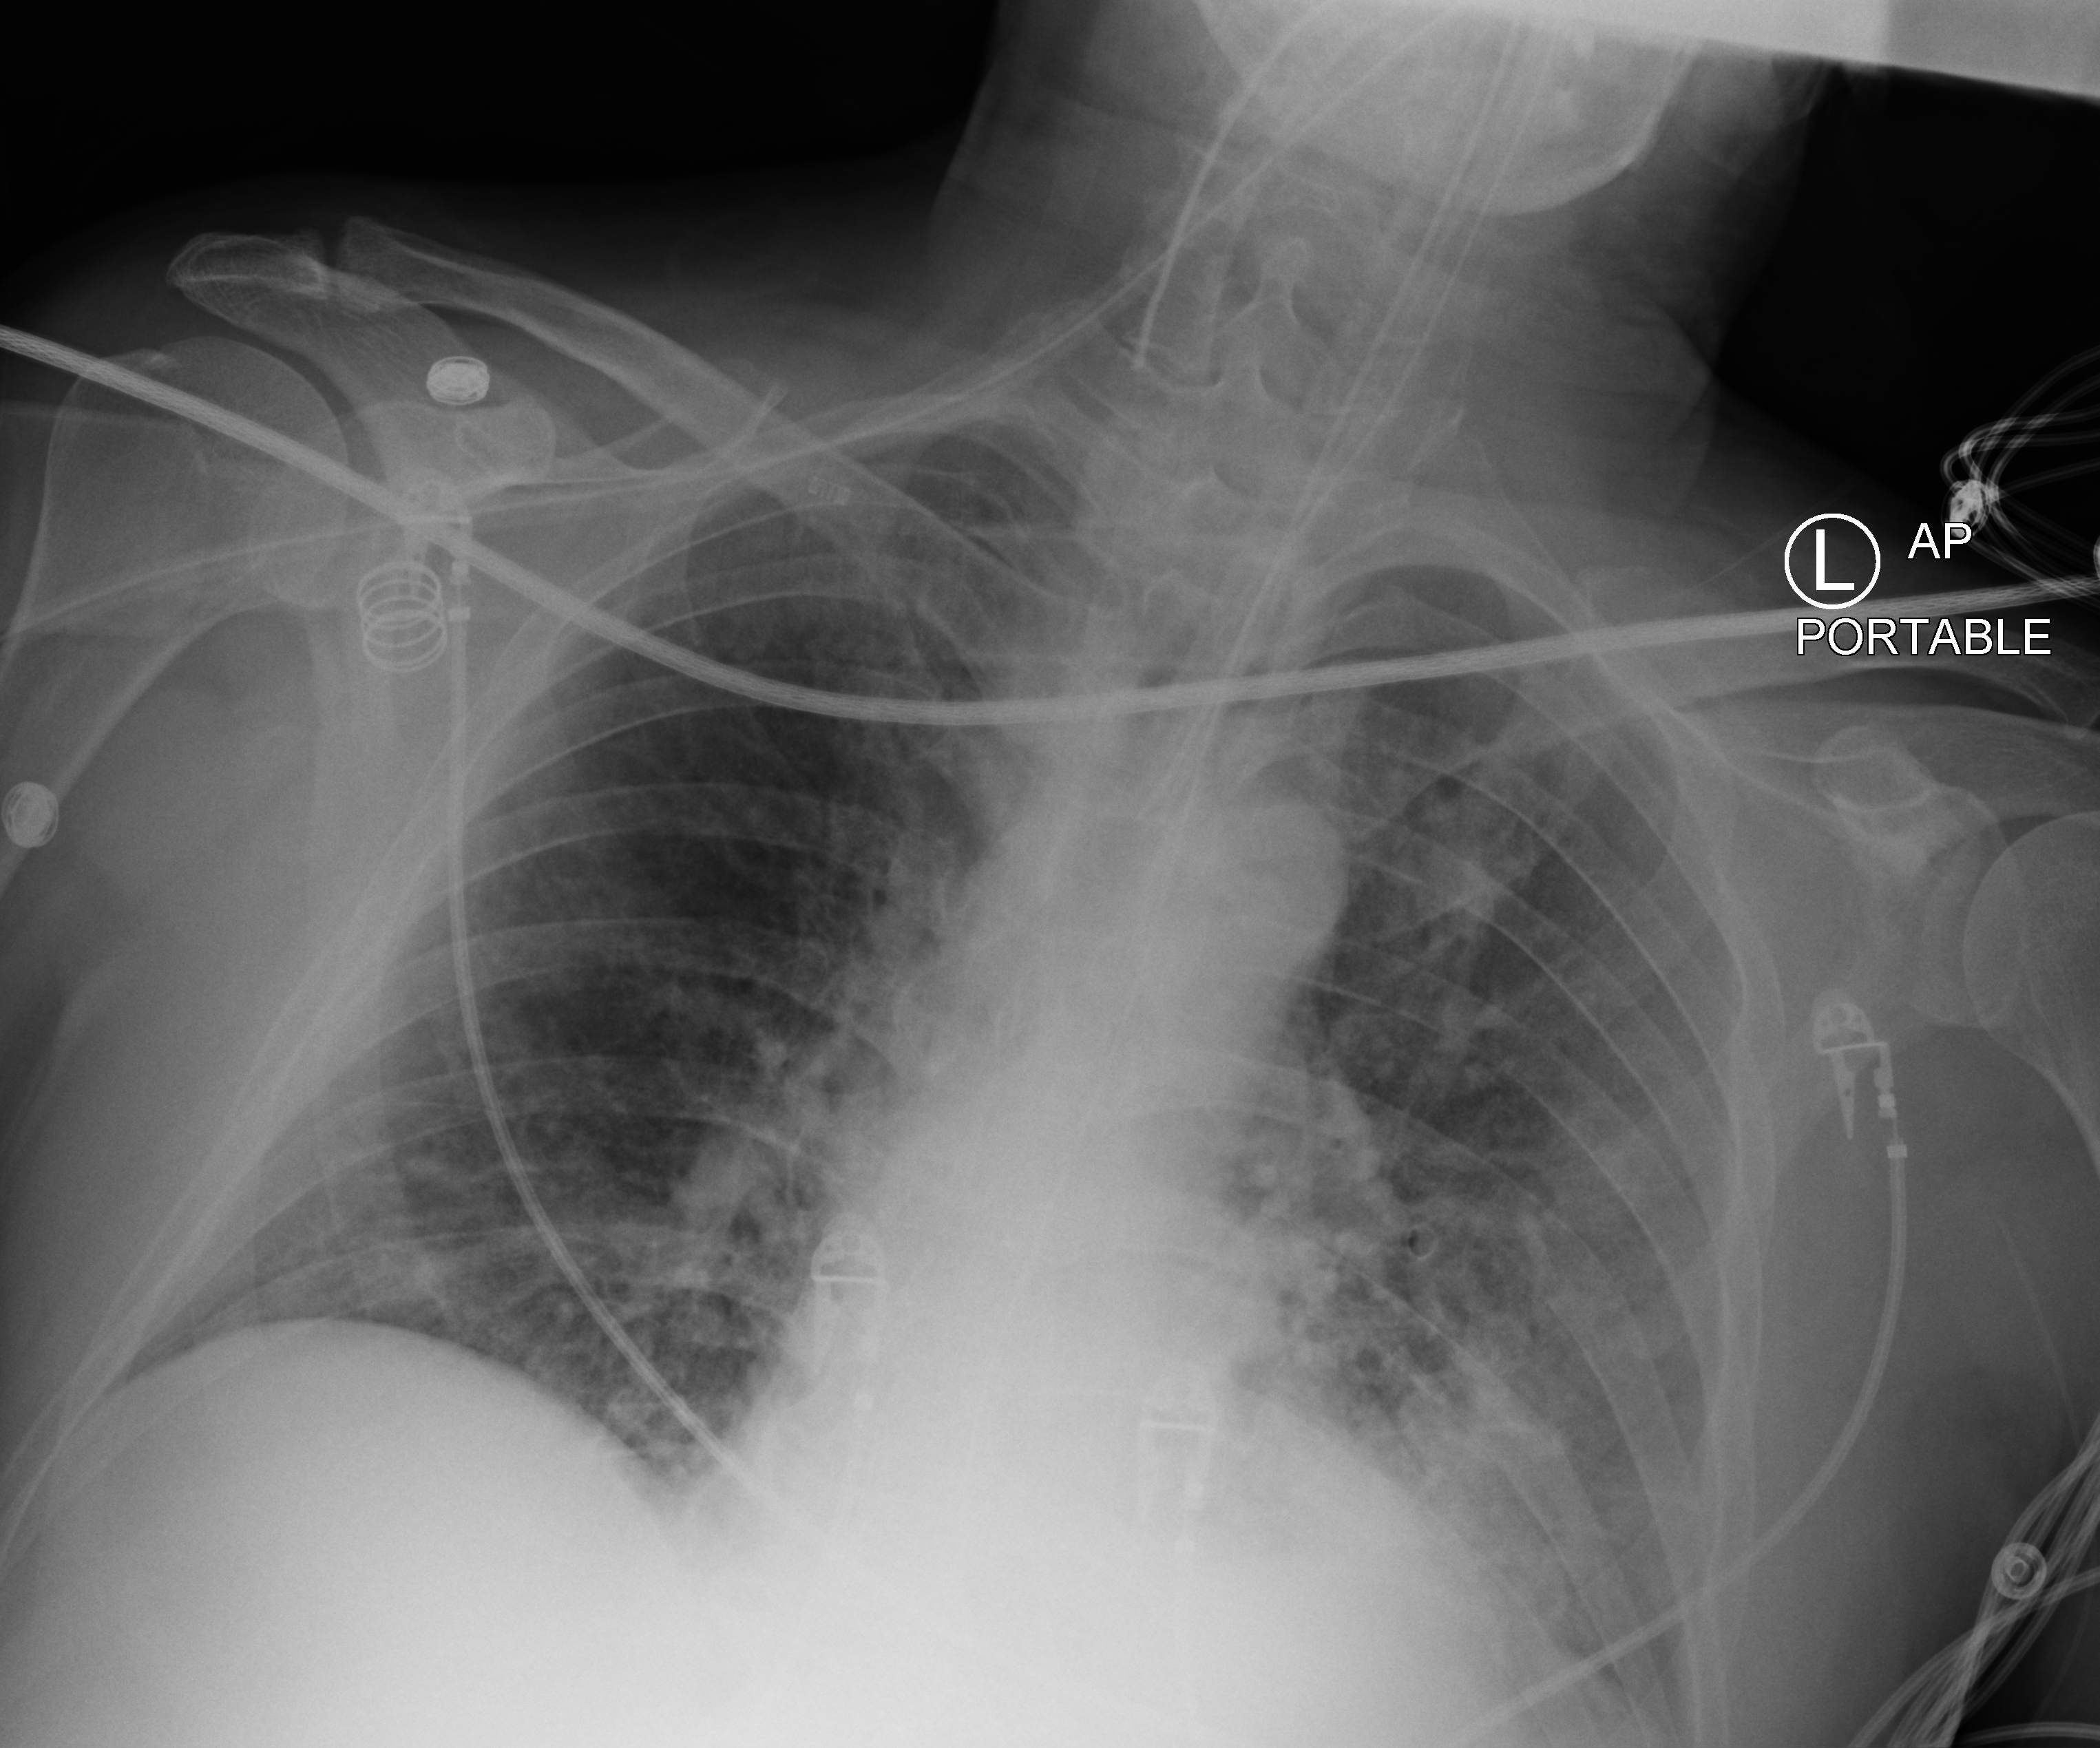
Chest X-ray (portable); anteroposterior (AP) projection. Male patient hospitalised with COVID-19, age 18–59 years.
Admission-level facts for this patient (not findings on this image; timing relative to this image not recorded):
- other chronic lung disease (admission record): no
- admitted to intensive care during this hospital stay: no